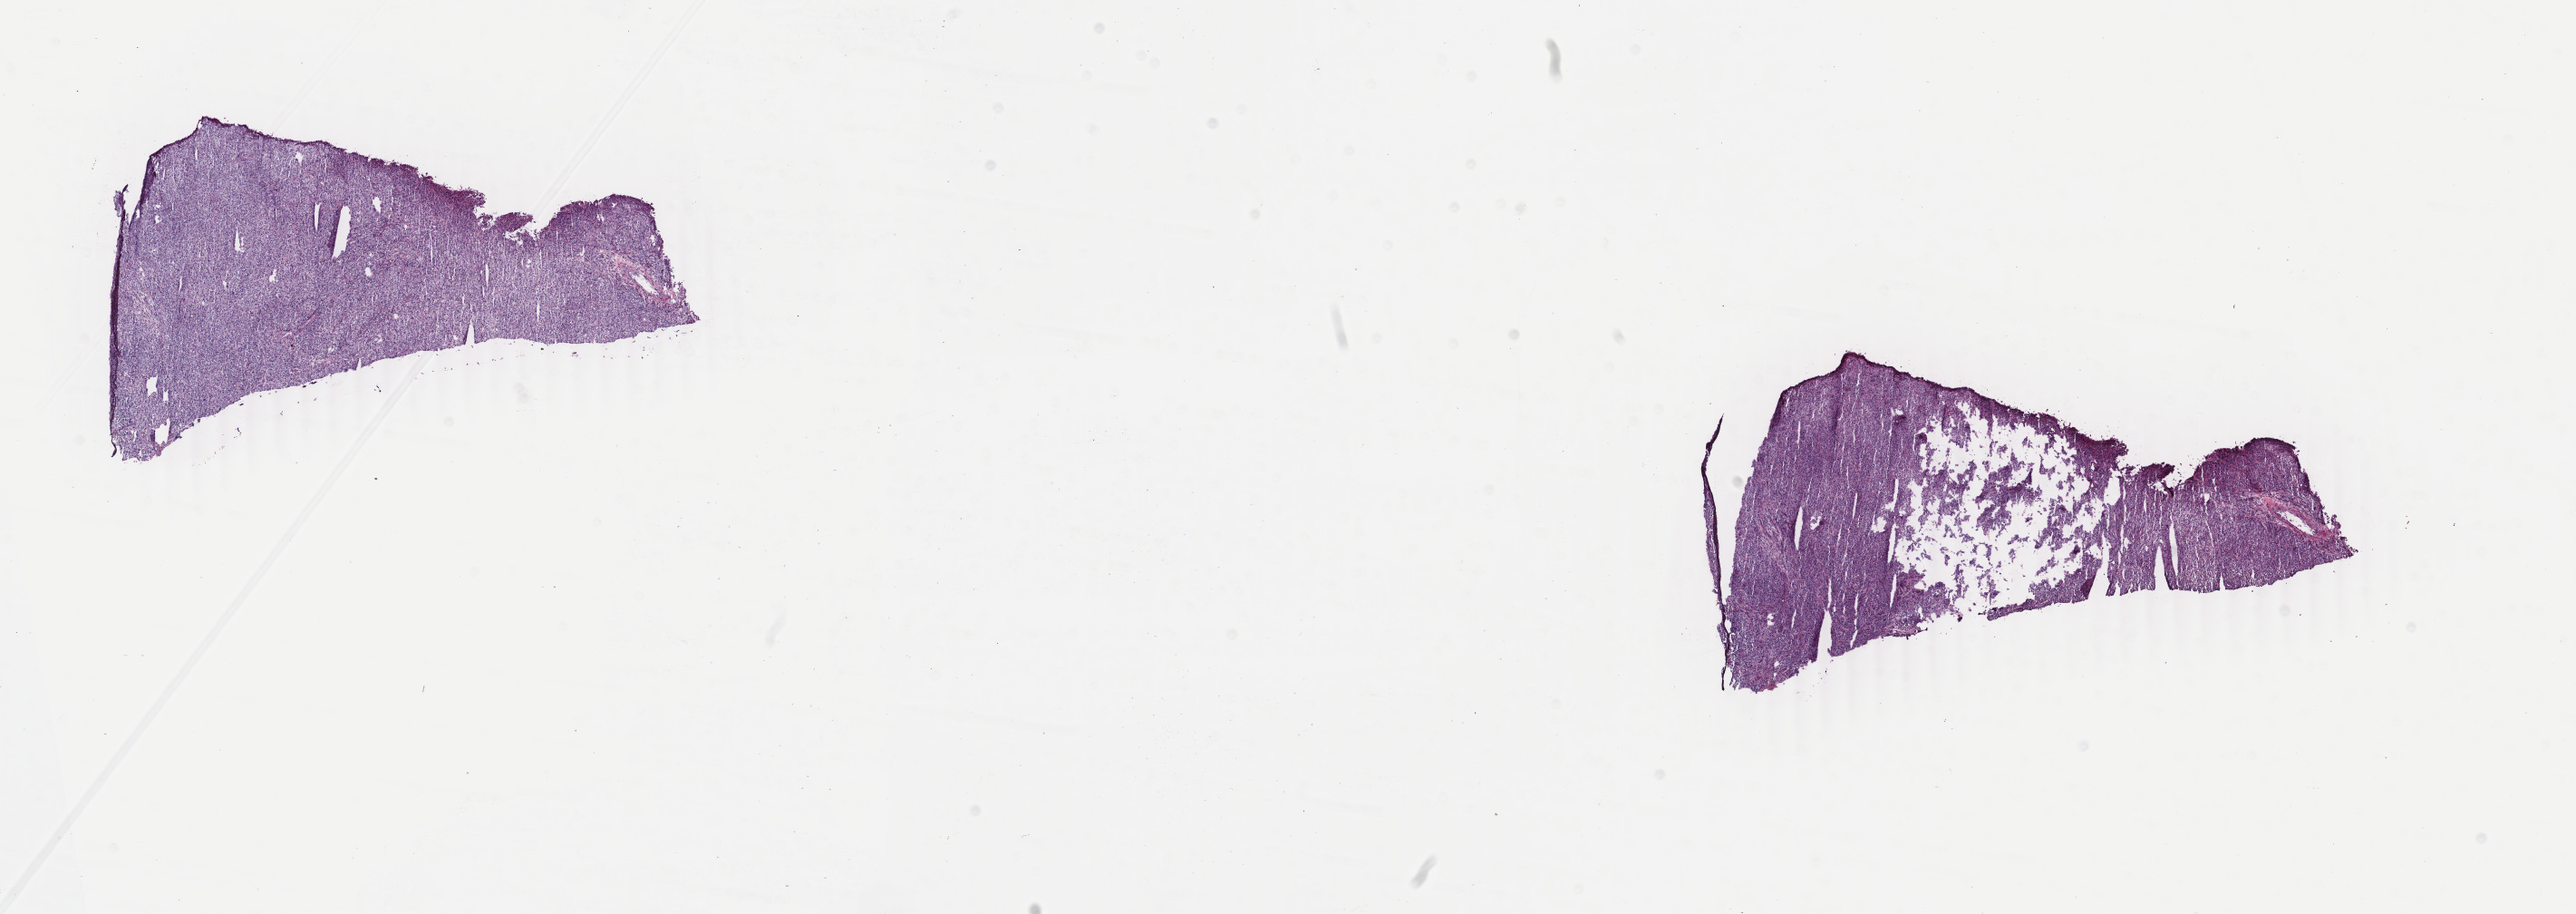
Digitized H&E-stained tissue section (whole slide), low-resolution overview of the scanned area, about 22.6 x 8.0 mm (from a 40x scan). Frozen section from the bottom of the tissue portion. Cervix, primary tumour sample. Female, age 21 years at initial diagnosis. Histologic grade: G3 (poorly differentiated). Pathologist review of this section (percent, as recorded): tumour cells 95%, tumour nuclei 95%, normal cells 0%, stromal cells 5%, necrosis 0%. Infiltration values recorded for this section: lymphocyte infiltration 30%, monocyte infiltration 0%, neutrophil infiltration 20%.
FIGO stage: IB2. Diagnosis: Squamous cell carcinoma, keratinizing, NOS (cervix uteri).